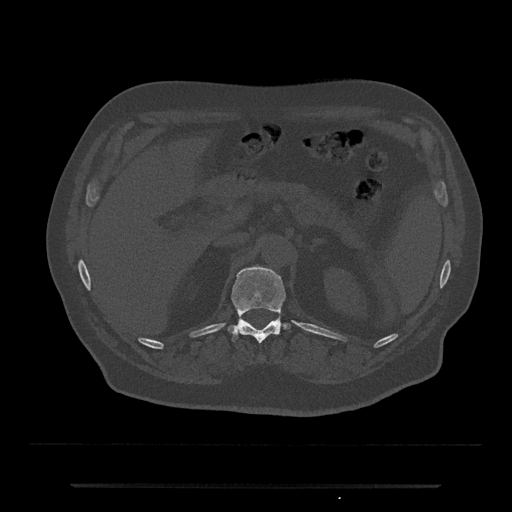
CT including the spine, one axial slice. Slice 590 of 797 in the series (ordered by position). Reconstruction kernel Br40s/3. Bone window (W 1800 / L 400 HU). 512 × 512 image matrix. Patient: male, 80 years. From the clinical record (not read from this slice): primary cancer: prostate; vertebrae with lytic lesions (as recorded): L1, T11.
Outlined on this slice (semi-automatic segmentation, software-assisted and operator-edited):
- T12 vertebra: bounding box (x1, y1, x2, y2) in pixels: (228, 267, 290, 344)